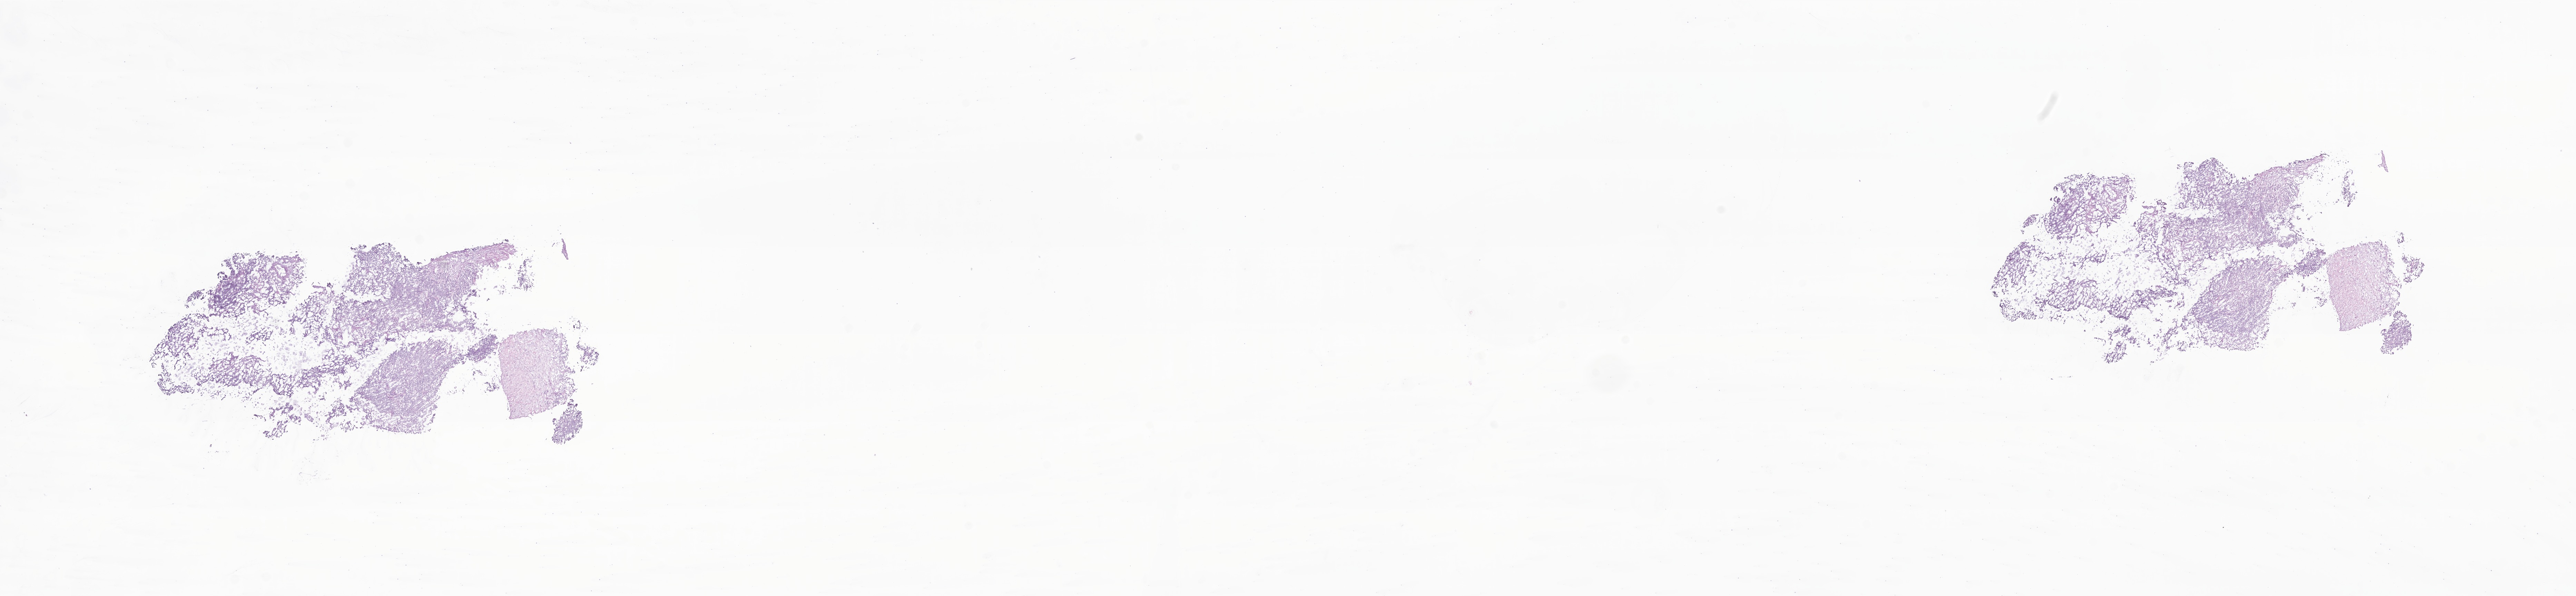
Whole-slide image, H&E stain of tumor tissue from the retroperitoneum, low-resolution overview of the scanned area, about 31.5 x 7.3 mm. Frozen section. Patient: female, age 37 months (3 years 1 month).
Recorded diagnosis: Rhabdomyosarcoma, NOS.